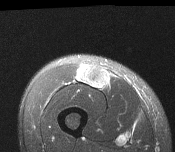
MRI of an extremity soft-tissue mass, one axial slice; slice 48 of 116 in the series (ordered by position); T2-weighted fat-saturated; MR volume resampled by the dataset authors to the PET/CT grid (not the native acquisition matrix); 3.27 mm slice thickness; 175 × 152 image matrix, field of view 171 × 148 mm. Male patient. From the clinical record (not read from this slice): histological type: pleiomorphic leiomyosarcoma; grade: intermediate; site of the primary tumour: right thigh.
Outlined on this slice (expert contour drawn on MRI and transferred to this co-registered scan by the dataset authors):
- gross tumour volume including surrounding oedema: box from (x=77, y=65) to (x=110, y=89) px